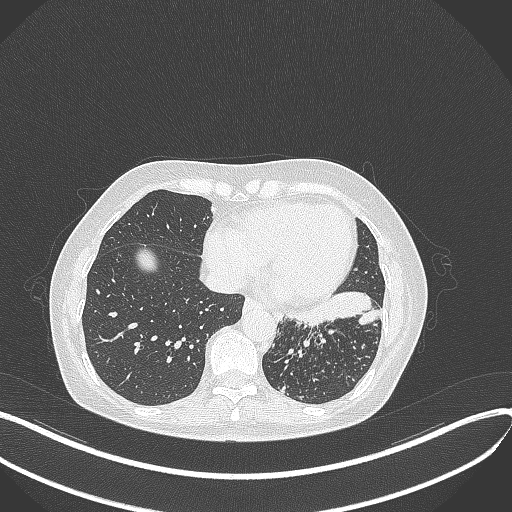
Chest CT, one axial slice; reconstruction kernel B70f; 100 kVp; lung window (W 1500 / L -600 HU); 512 × 512 image matrix. Patient: female, 63 years. Case-level facts recorded for this patient, not image findings: clinical TNM (as recorded): T1b N0 M0; histopathological grade: G2-3.
Outlined on this slice (bounding box drawn by a radiologist):
- lung tumour (recorded histology: adenocarcinoma): bounding box (x1, y1, x2, y2) in pixels: (282, 287, 386, 337)